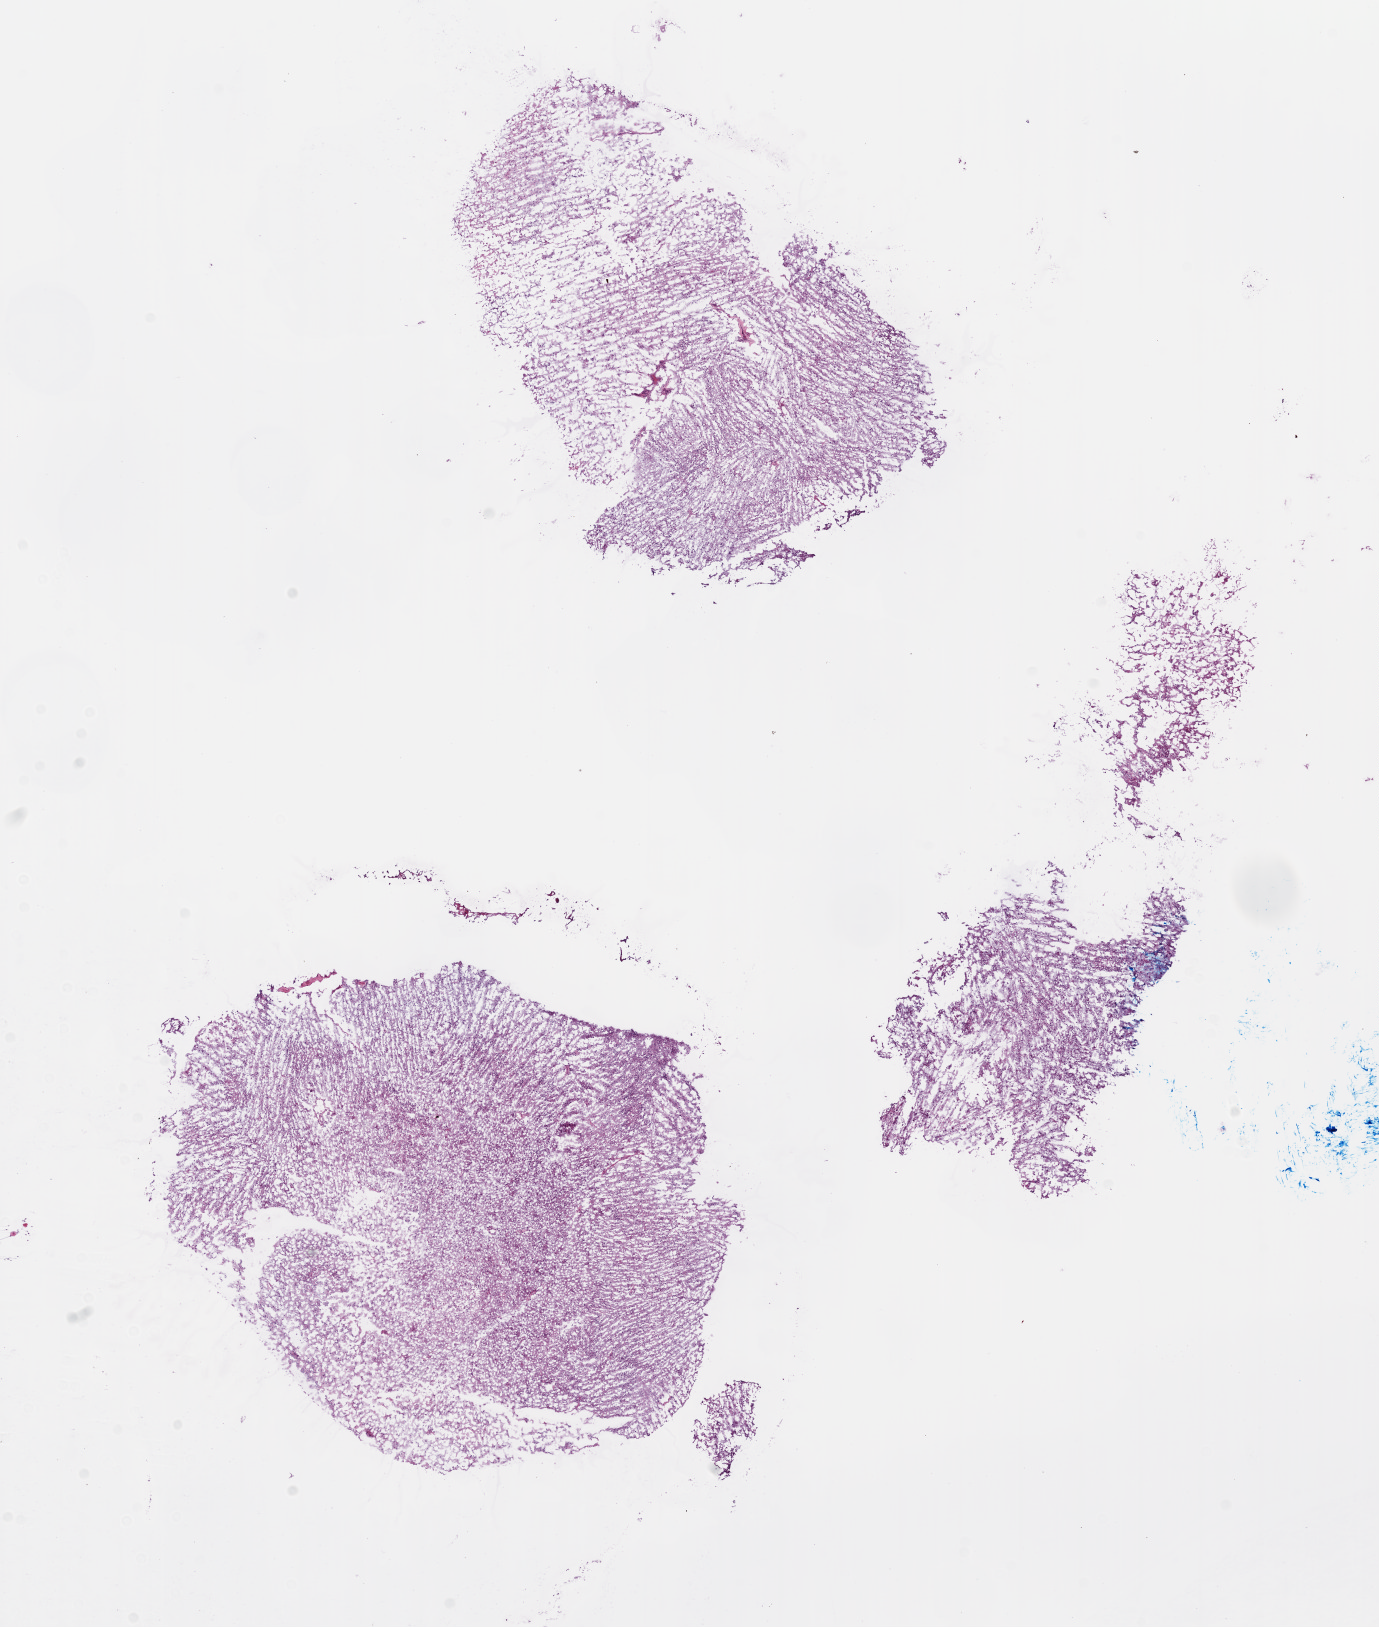
Digitized H&E-stained tissue section (whole slide), whole scanned area (about 11.1 x 13.1 mm, acquisition: 20x scan) shown as a low-resolution overview; frozen section from the top of the tissue portion; primary tumour sample from the brain. Patient: male, age at initial diagnosis 65 years.
Diagnosis: Glioblastoma.